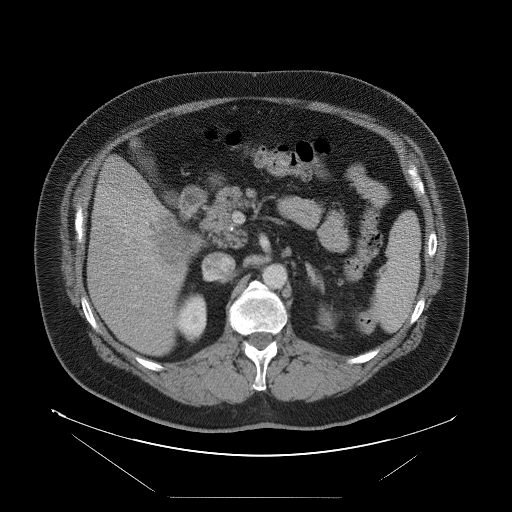
Contrast-enhanced abdominal CT, one axial slice. Position 46 of 114 along the scan axis. 120 kVp. Intravenous contrast given. Soft-tissue window (W 400 / L 40 HU). 512 × 512 image matrix, field of view 500 × 500 mm. Male patient, age 61 years. Case-level facts recorded for this patient, not image findings: diagnosis: colorectal cancer liver metastases, imaged before liver resection; multiple liver metastases: no; largest metastasis: 6.5 cm; chemotherapy before resection: no.
Structures marked on this image (manually delineated by an expert):
- liver: bounding box (x1, y1, x2, y2) in pixels: (89, 157, 202, 356)
- liver metastasis: (158, 216, 199, 270)